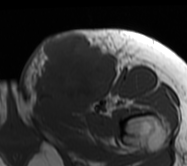
MRI of an extremity soft-tissue mass, one axial slice. Slice 25 of 62 in the series (ordered by position). MR volume resampled by the dataset authors to the PET/CT grid (not the native acquisition matrix). 3.27 mm slice thickness. 187 × 166 image matrix, field of view 183 × 162 mm. Female patient. Case-level facts recorded for this patient, not image findings: histological type: leiomyosarcoma; grade: high; site of the primary tumour: groin.
Outlined on this slice (expert contour drawn on MRI and transferred to this co-registered scan by the dataset authors):
- gross tumour volume including surrounding oedema: box from (x=20, y=28) to (x=135, y=111) px
- gross tumour volume (mass): (x=34, y=33)–(x=115, y=109)